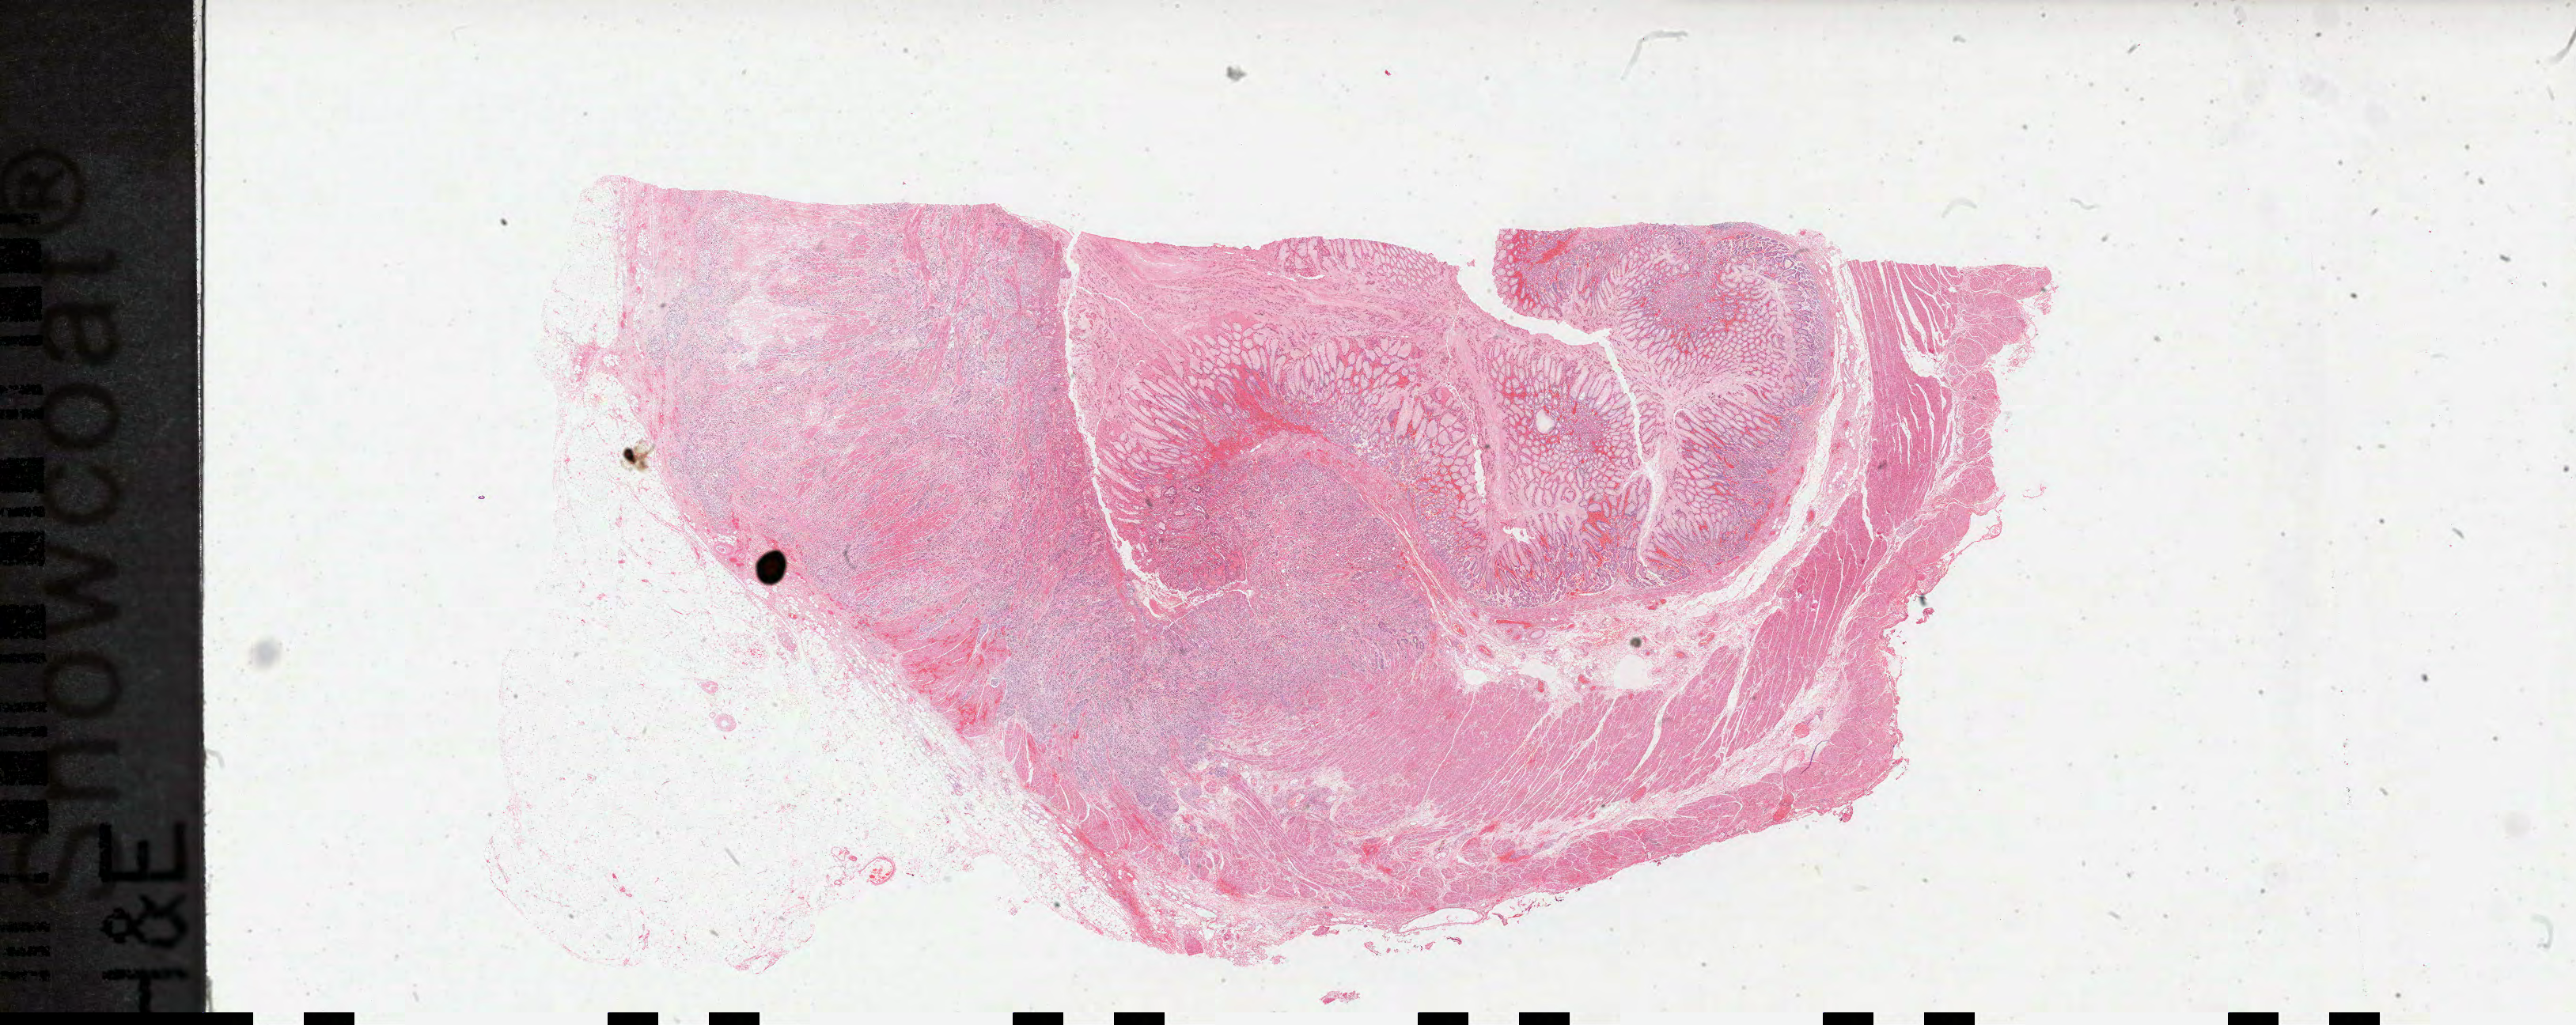
H&E whole-slide image, a low-resolution overview of the entire scanned area, about 52.7 x 21.0 mm. Formalin-fixed paraffin-embedded (FFPE) diagnostic section. Sample: primary tumour, esophagus. Patient: male, age at initial diagnosis 65 years. Histologic grade: G3 (poorly differentiated).
Lymph nodes positive (case pathology): 12 of 24 examined. TNM: T3 N3 MX. Diagnosis: Adenocarcinoma, NOS. AJCC pathologic stage: IIIC (7th edition).